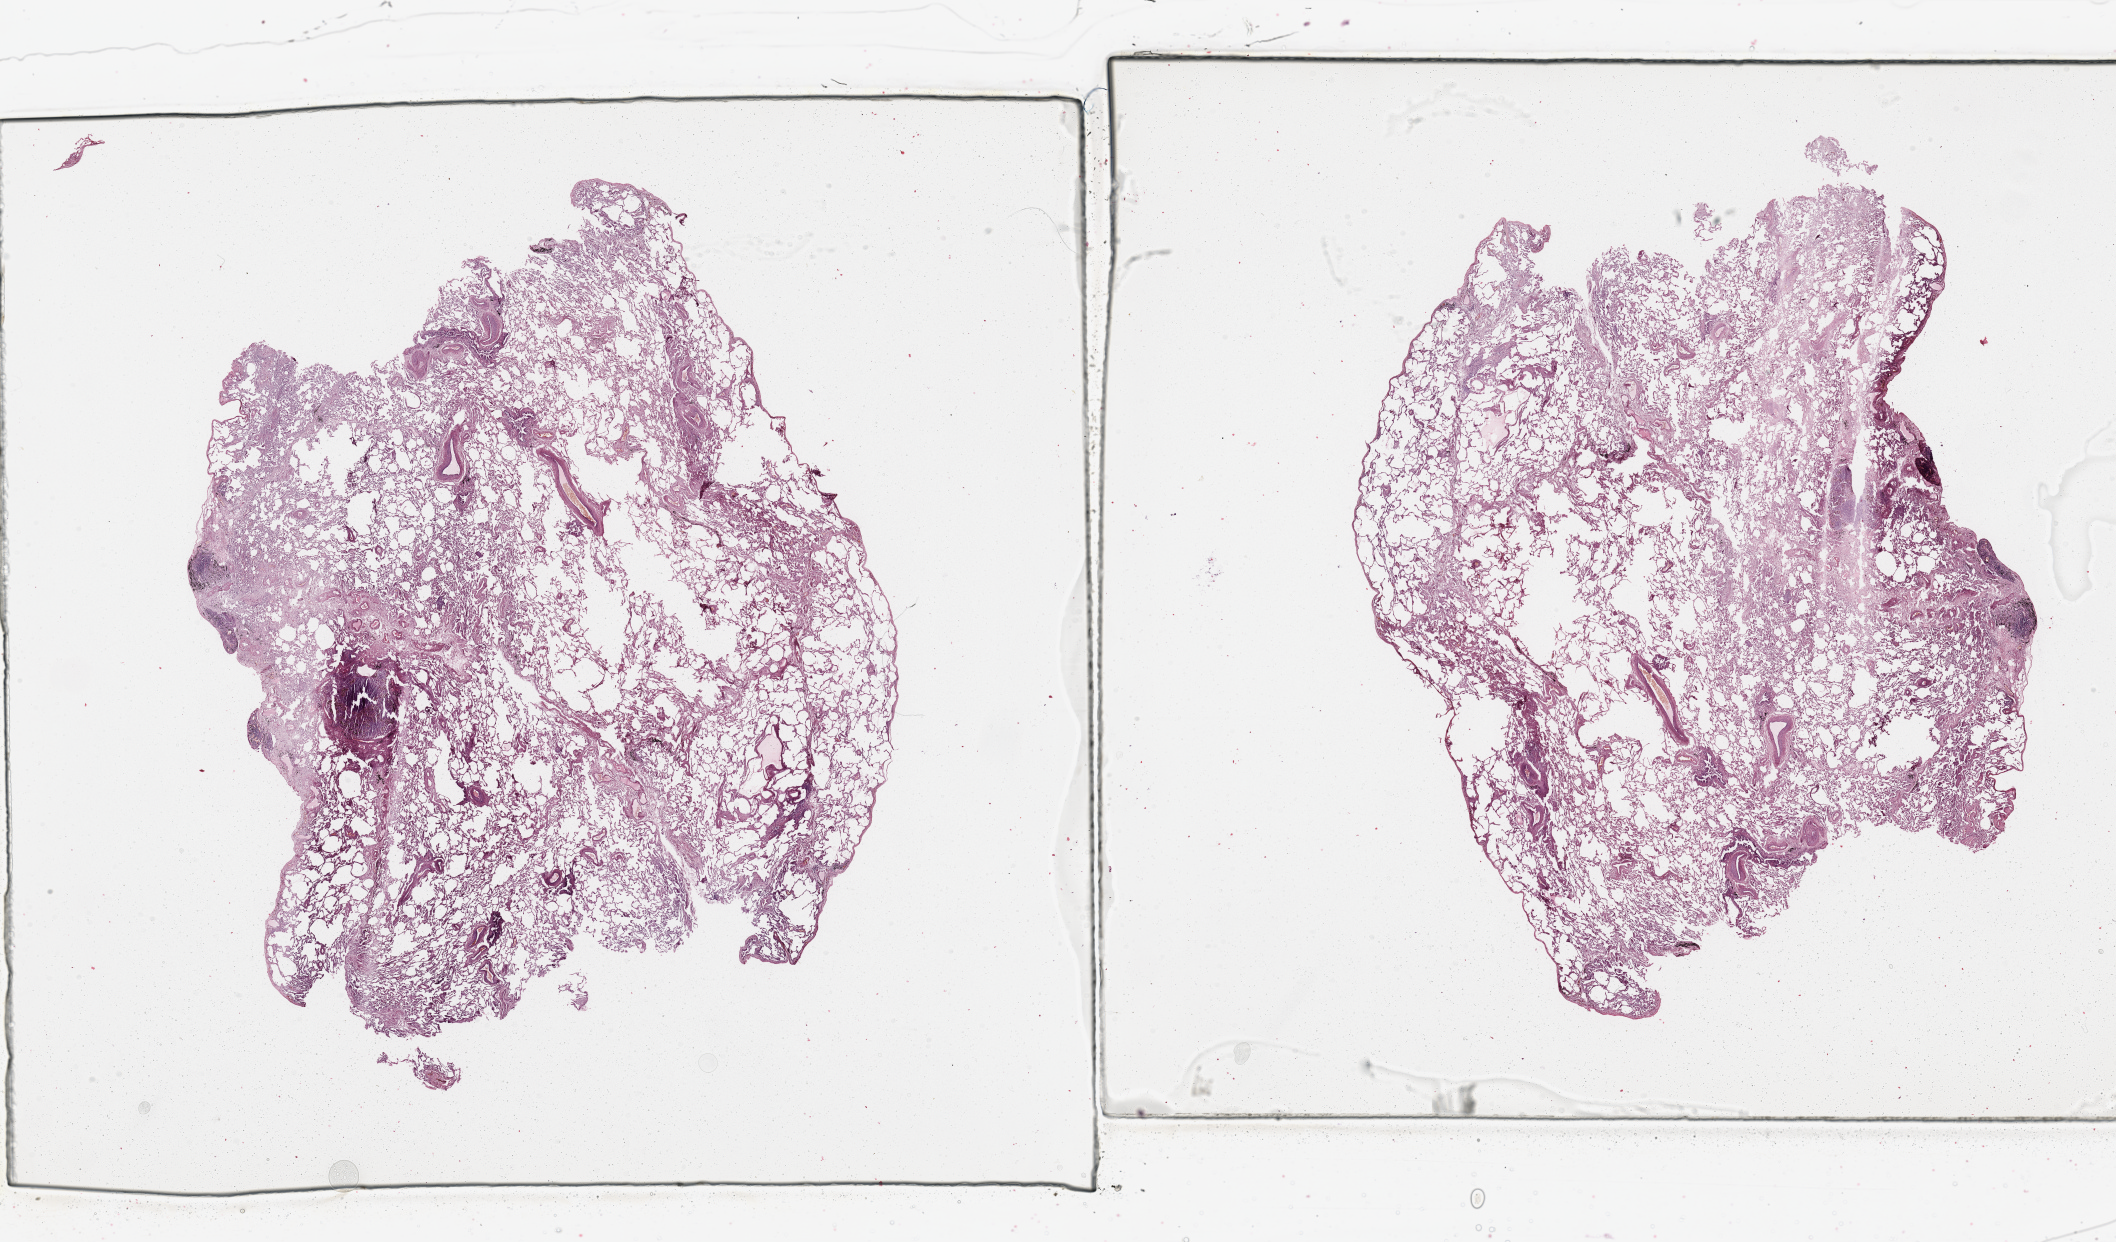
Digitized Hematoxylin and eosin (H&E) stained tissue section (whole slide), whole scanned area (about 33.5 x 19.6 mm, slide scanned at 20x) shown as a low-resolution overview; normal (non-tumour) tissue sample, sampled site: lung. 60-year-old male patient.
This section: normal (non-tumour) tissue from the same patient. Patient diagnosis: Squamous cell carcinoma, NOS.